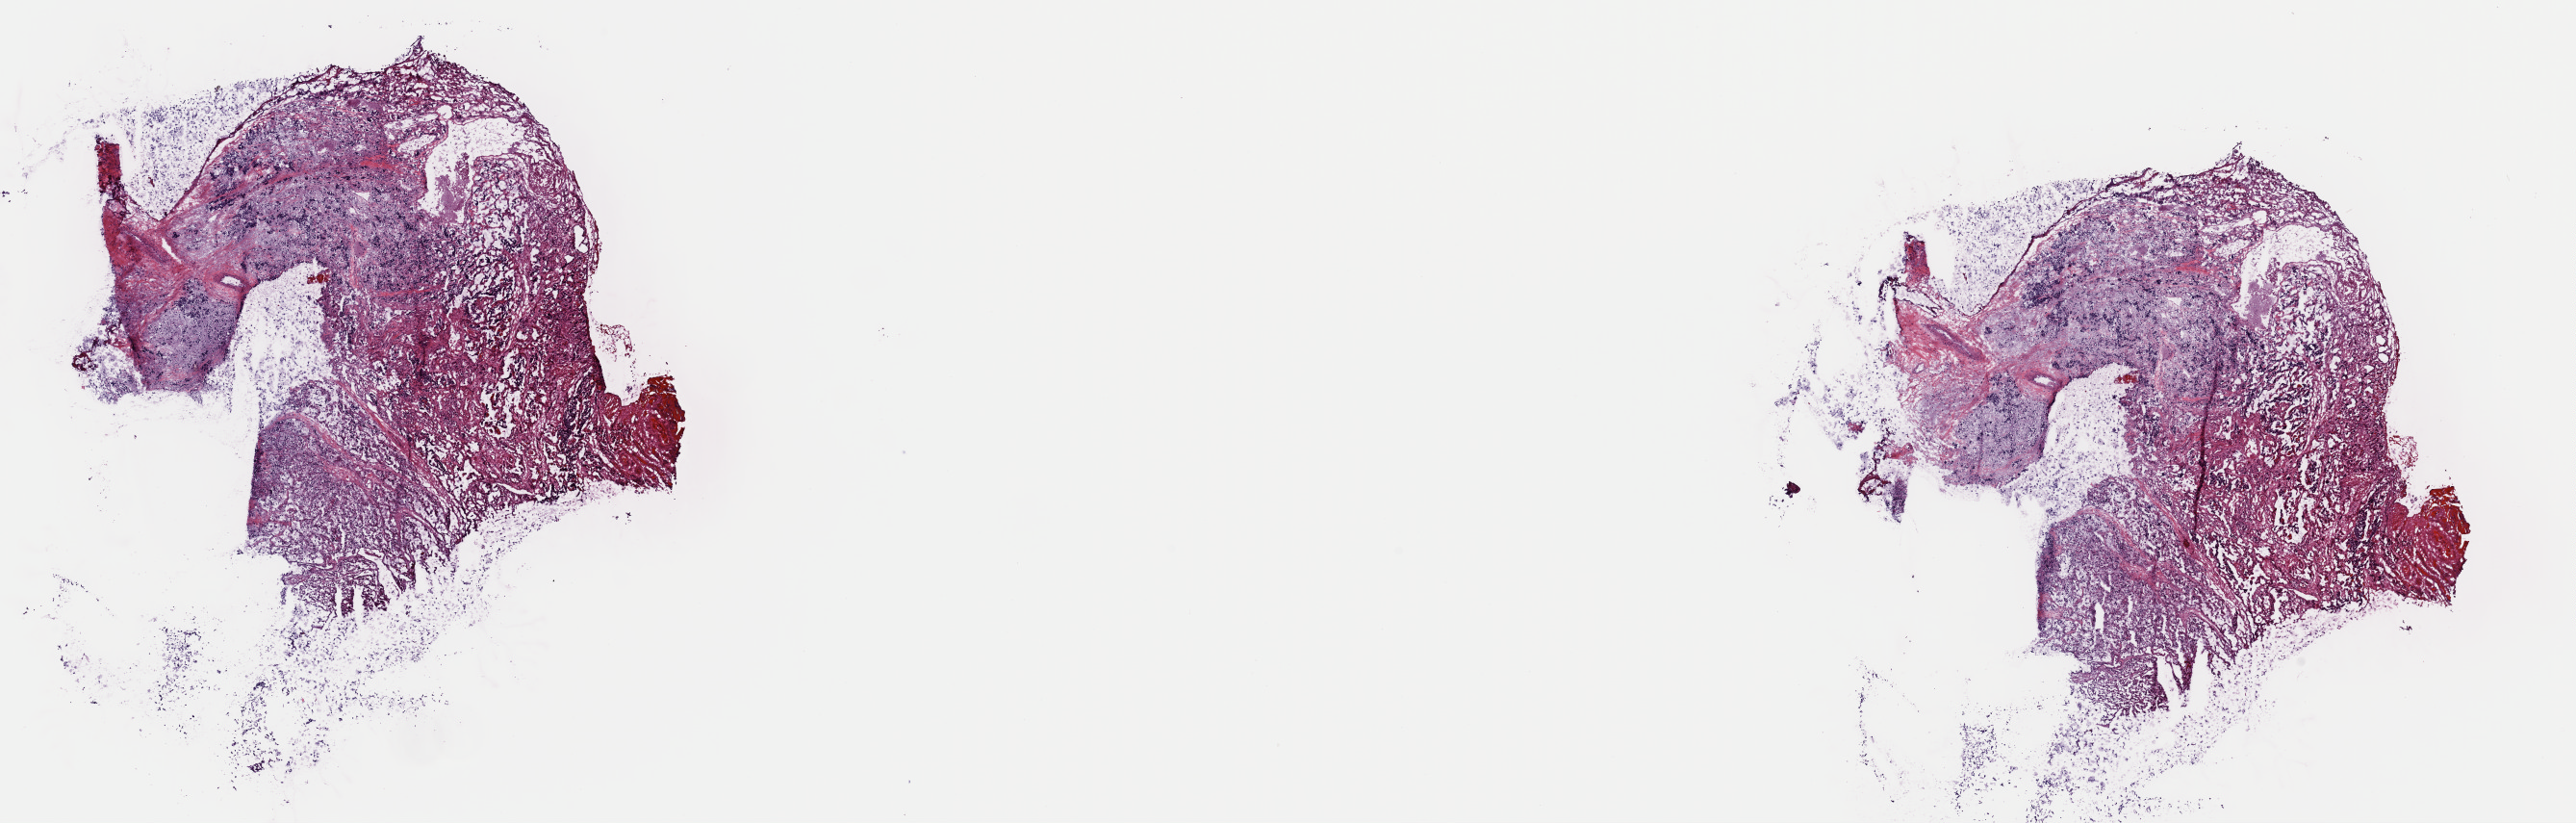
H&E-stained whole-slide image — shown as a low-resolution overview of the whole scanned area (about 21.1 x 6.8 mm, slide scanned at 40x); frozen section from the top of the tissue portion; primary tumour sample from the spinal cord, cranial nerves, and other parts of central nervous system. Male patient; age at initial diagnosis 55 years. Composition of this section per pathologist review: tumour cells 100%, tumour nuclei 75%, normal cells 0%, stromal cells 0%, necrosis 0%. Inflammatory infiltration, as recorded: lymphocyte infiltration 1%, monocyte infiltration 0%, neutrophil infiltration 0%.
- pathologic diagnosis: Paraganglioma, malignant